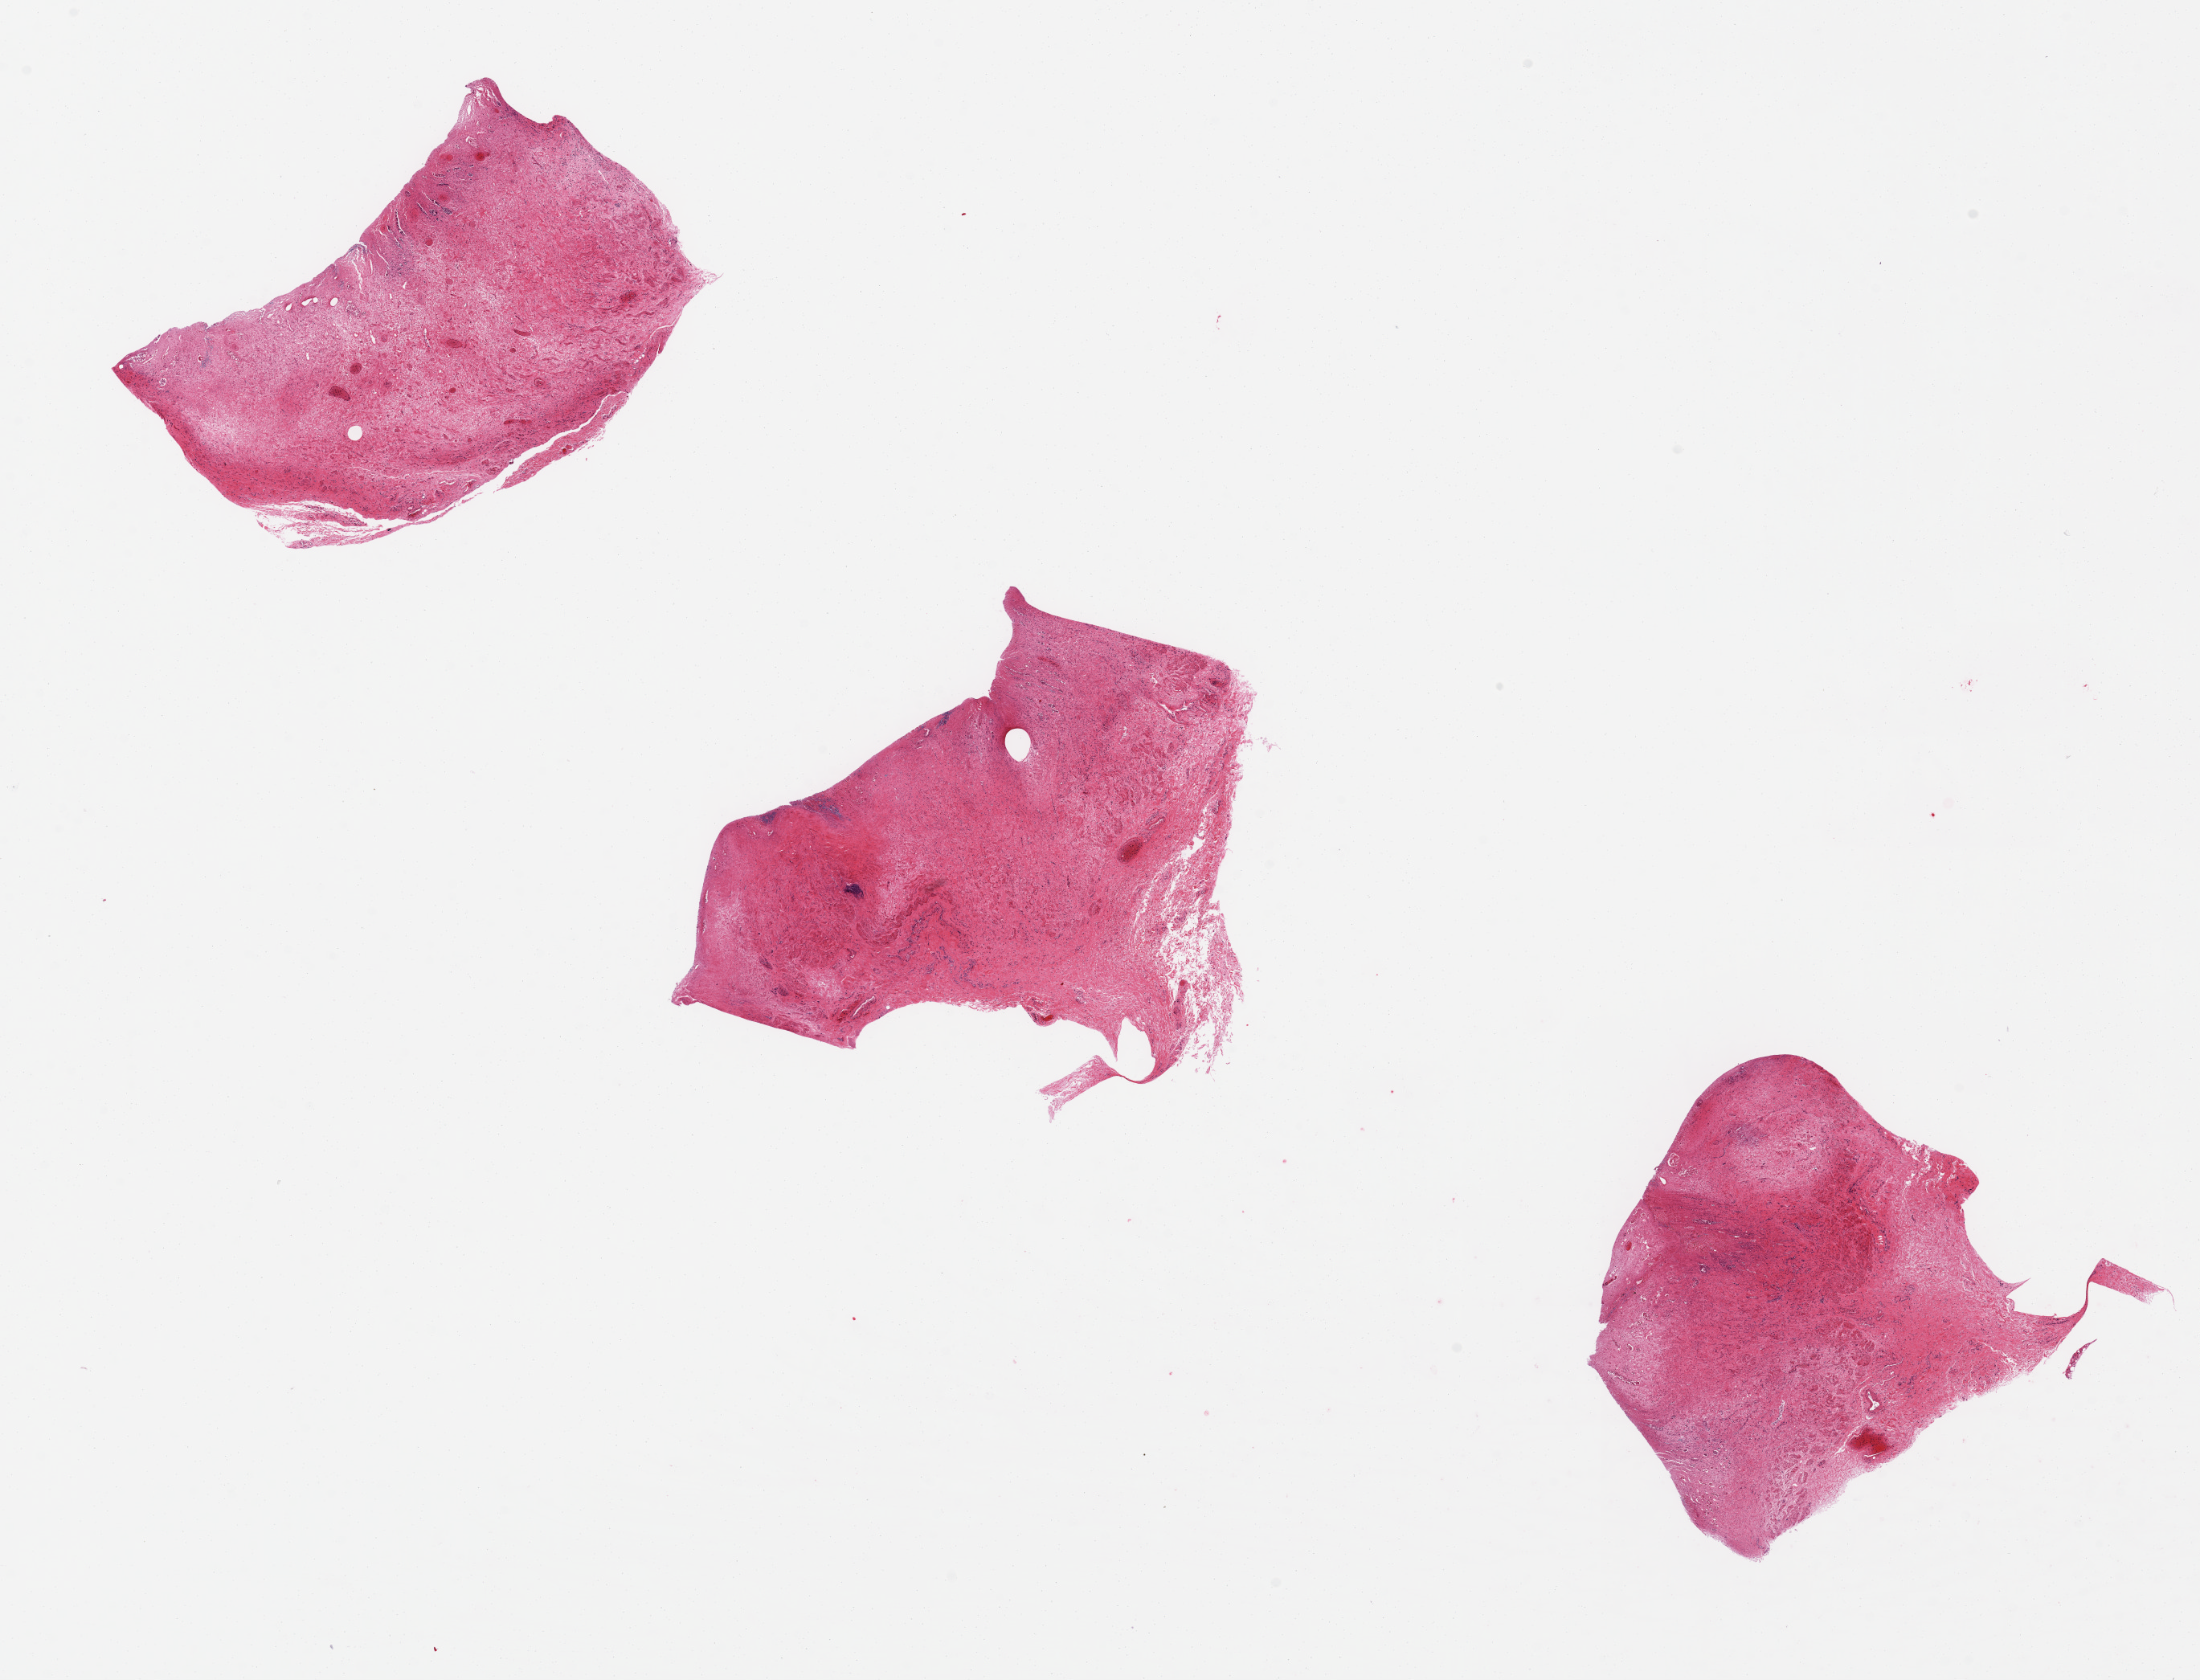
Hematoxylin and eosin (H&E) whole-slide image — a low-resolution overview of the entire scanned area, about 21.7 x 16.5 mm. PAXgene-fixed, paraffin-embedded tissue. Target tissue: esophageal mucous membrane. Tissue donor sample. Male donor.
Reviewer comment on this tissue sample: Three ~5mm tissue fragments. ? origin. No mucosa seen.